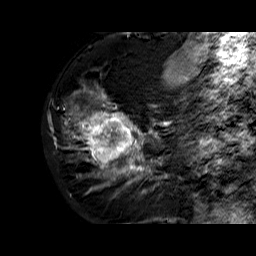
Breast MRI (dynamic contrast-enhanced), one sagittal slice; dynamic contrast-enhanced series, time point 2 of 6 at this slice position (early post-contrast); 1.5 T; TE 6.3 ms, TR 32.4 ms; 4 mm slice thickness; 256 × 256 image matrix. Female patient. Case-level facts recorded for this patient, not image findings: setting: breast cancer imaged before/during neoadjuvant chemotherapy; receptor status: HR-positive, HER2-negative.
Structures marked on this image (semi-automatically segmented with operator editing):
- analysis volume of interest (the breast-tissue region the enhancement analysis was run in; not a lesion): bounding box [x1, y1, x2, y2] px = [68, 72, 177, 183]
- tumour enhancement mask (voxels above the 100 % enhancement threshold inside the analysis volume of interest): [73, 92, 168, 183]